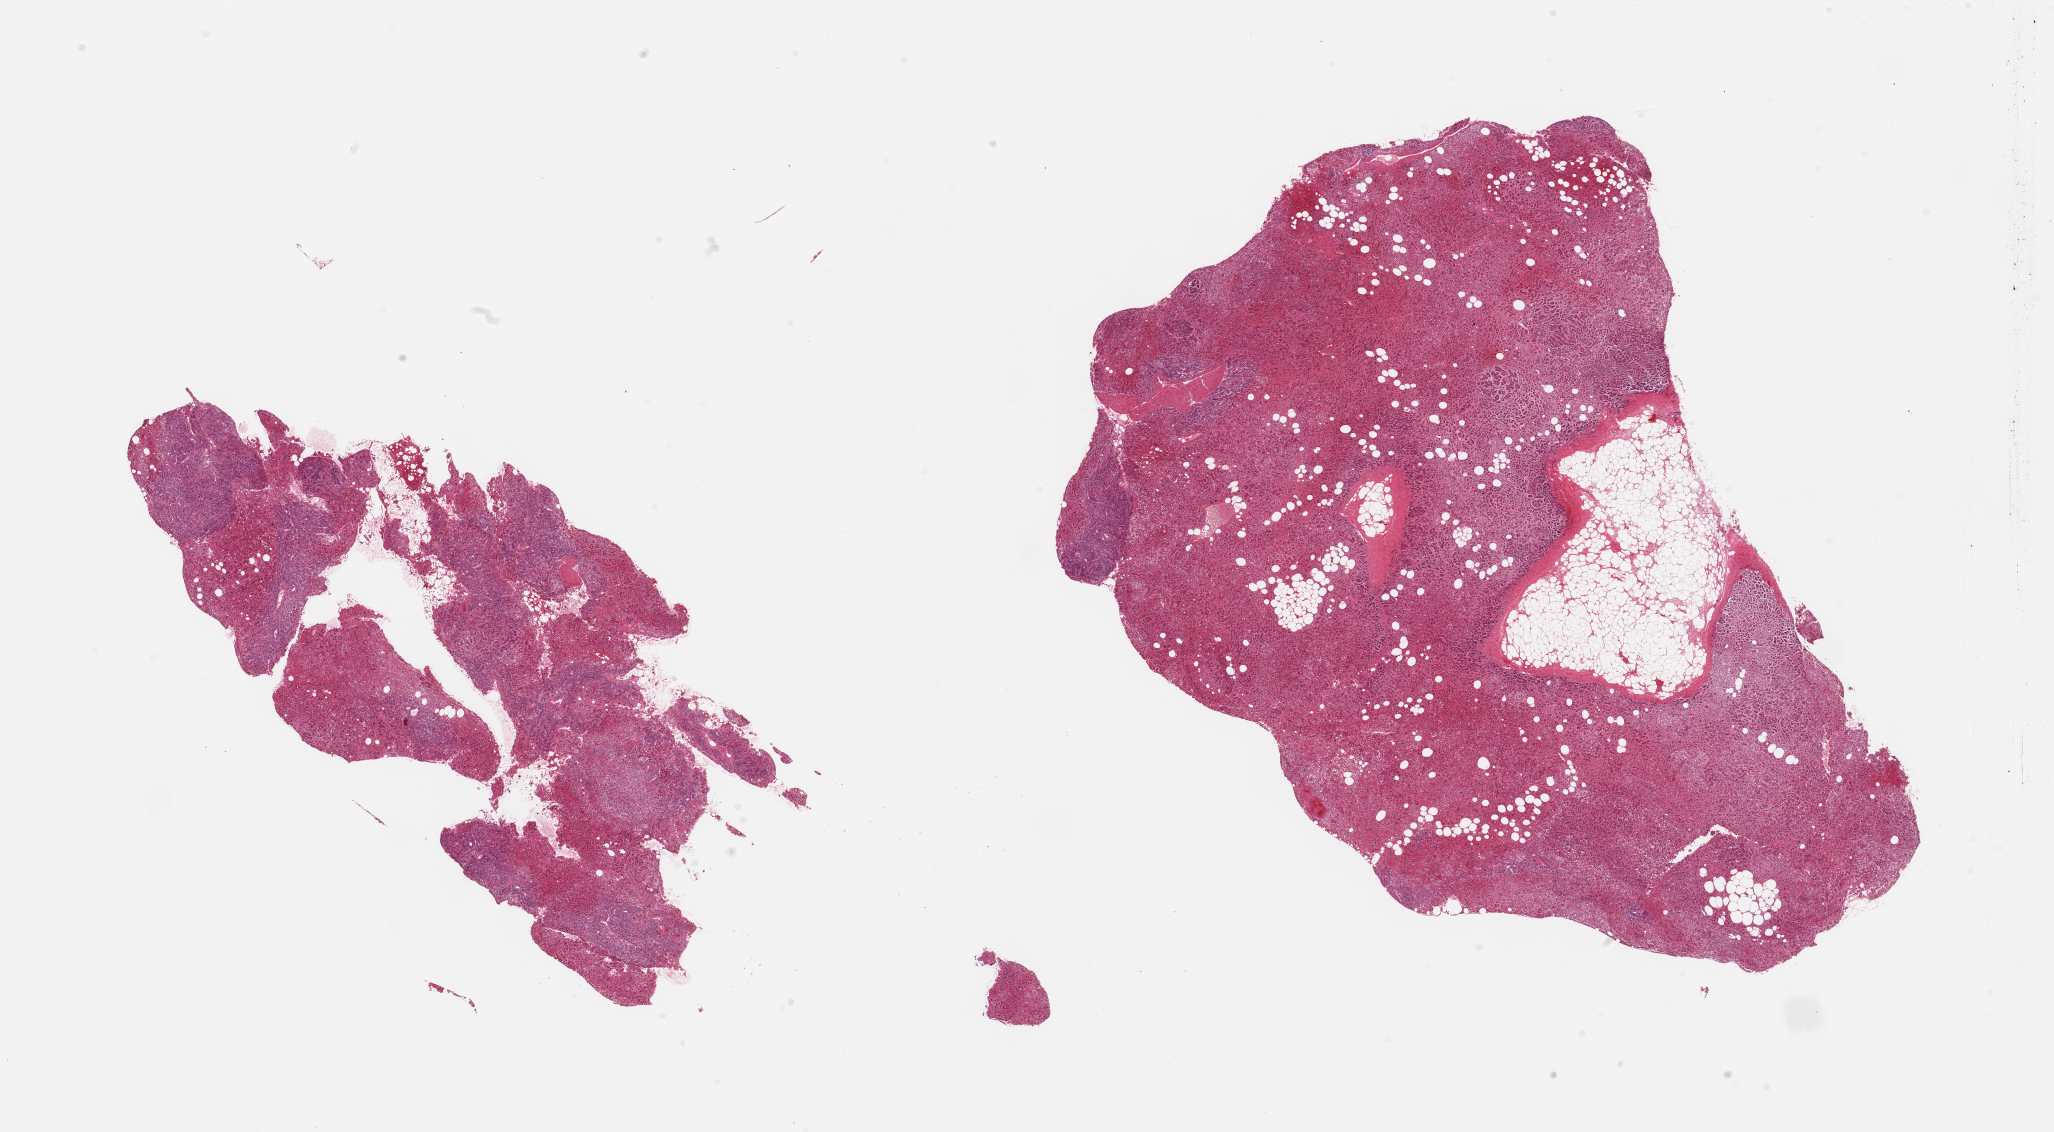
Hematoxylin and eosin (H&E) whole-slide image, a low-resolution overview of the entire scanned area, about 32.5 x 17.9 mm (slide scanned at 20x). PAXgene-fixed, paraffin-embedded tissue. Section of adrenal gland (target tissue). Donor tissue sample. Donor: male.
Review note (as recorded): 2 pieces; ? medullary hyperplasia.